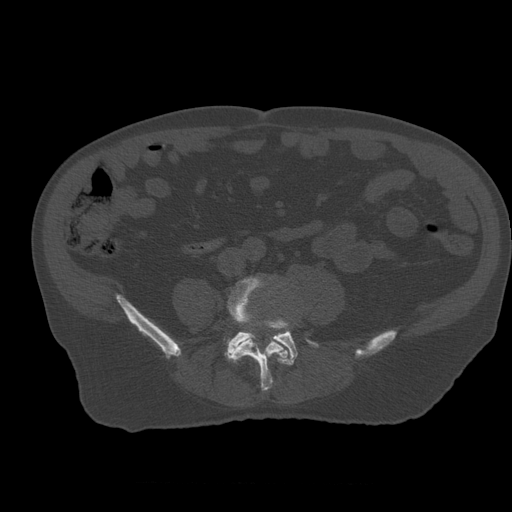
CT including the spine, one axial slice. Position 154 of 399 along the scan axis. Reconstruction kernel STANDARD. 120 kVp. Bone window (W 1800 / L 400 HU). 1.25 mm slice thickness. 512 × 512 image matrix. Patient age 73 years. Case-level facts recorded for this patient, not image findings: primary cancer: prostate.
Structures marked on this image (semi-automatically segmented with operator editing):
- L4 vertebra: box from (x=224, y=277) to (x=288, y=392) px
- L5 vertebra: (x=226, y=321)–(x=317, y=366)